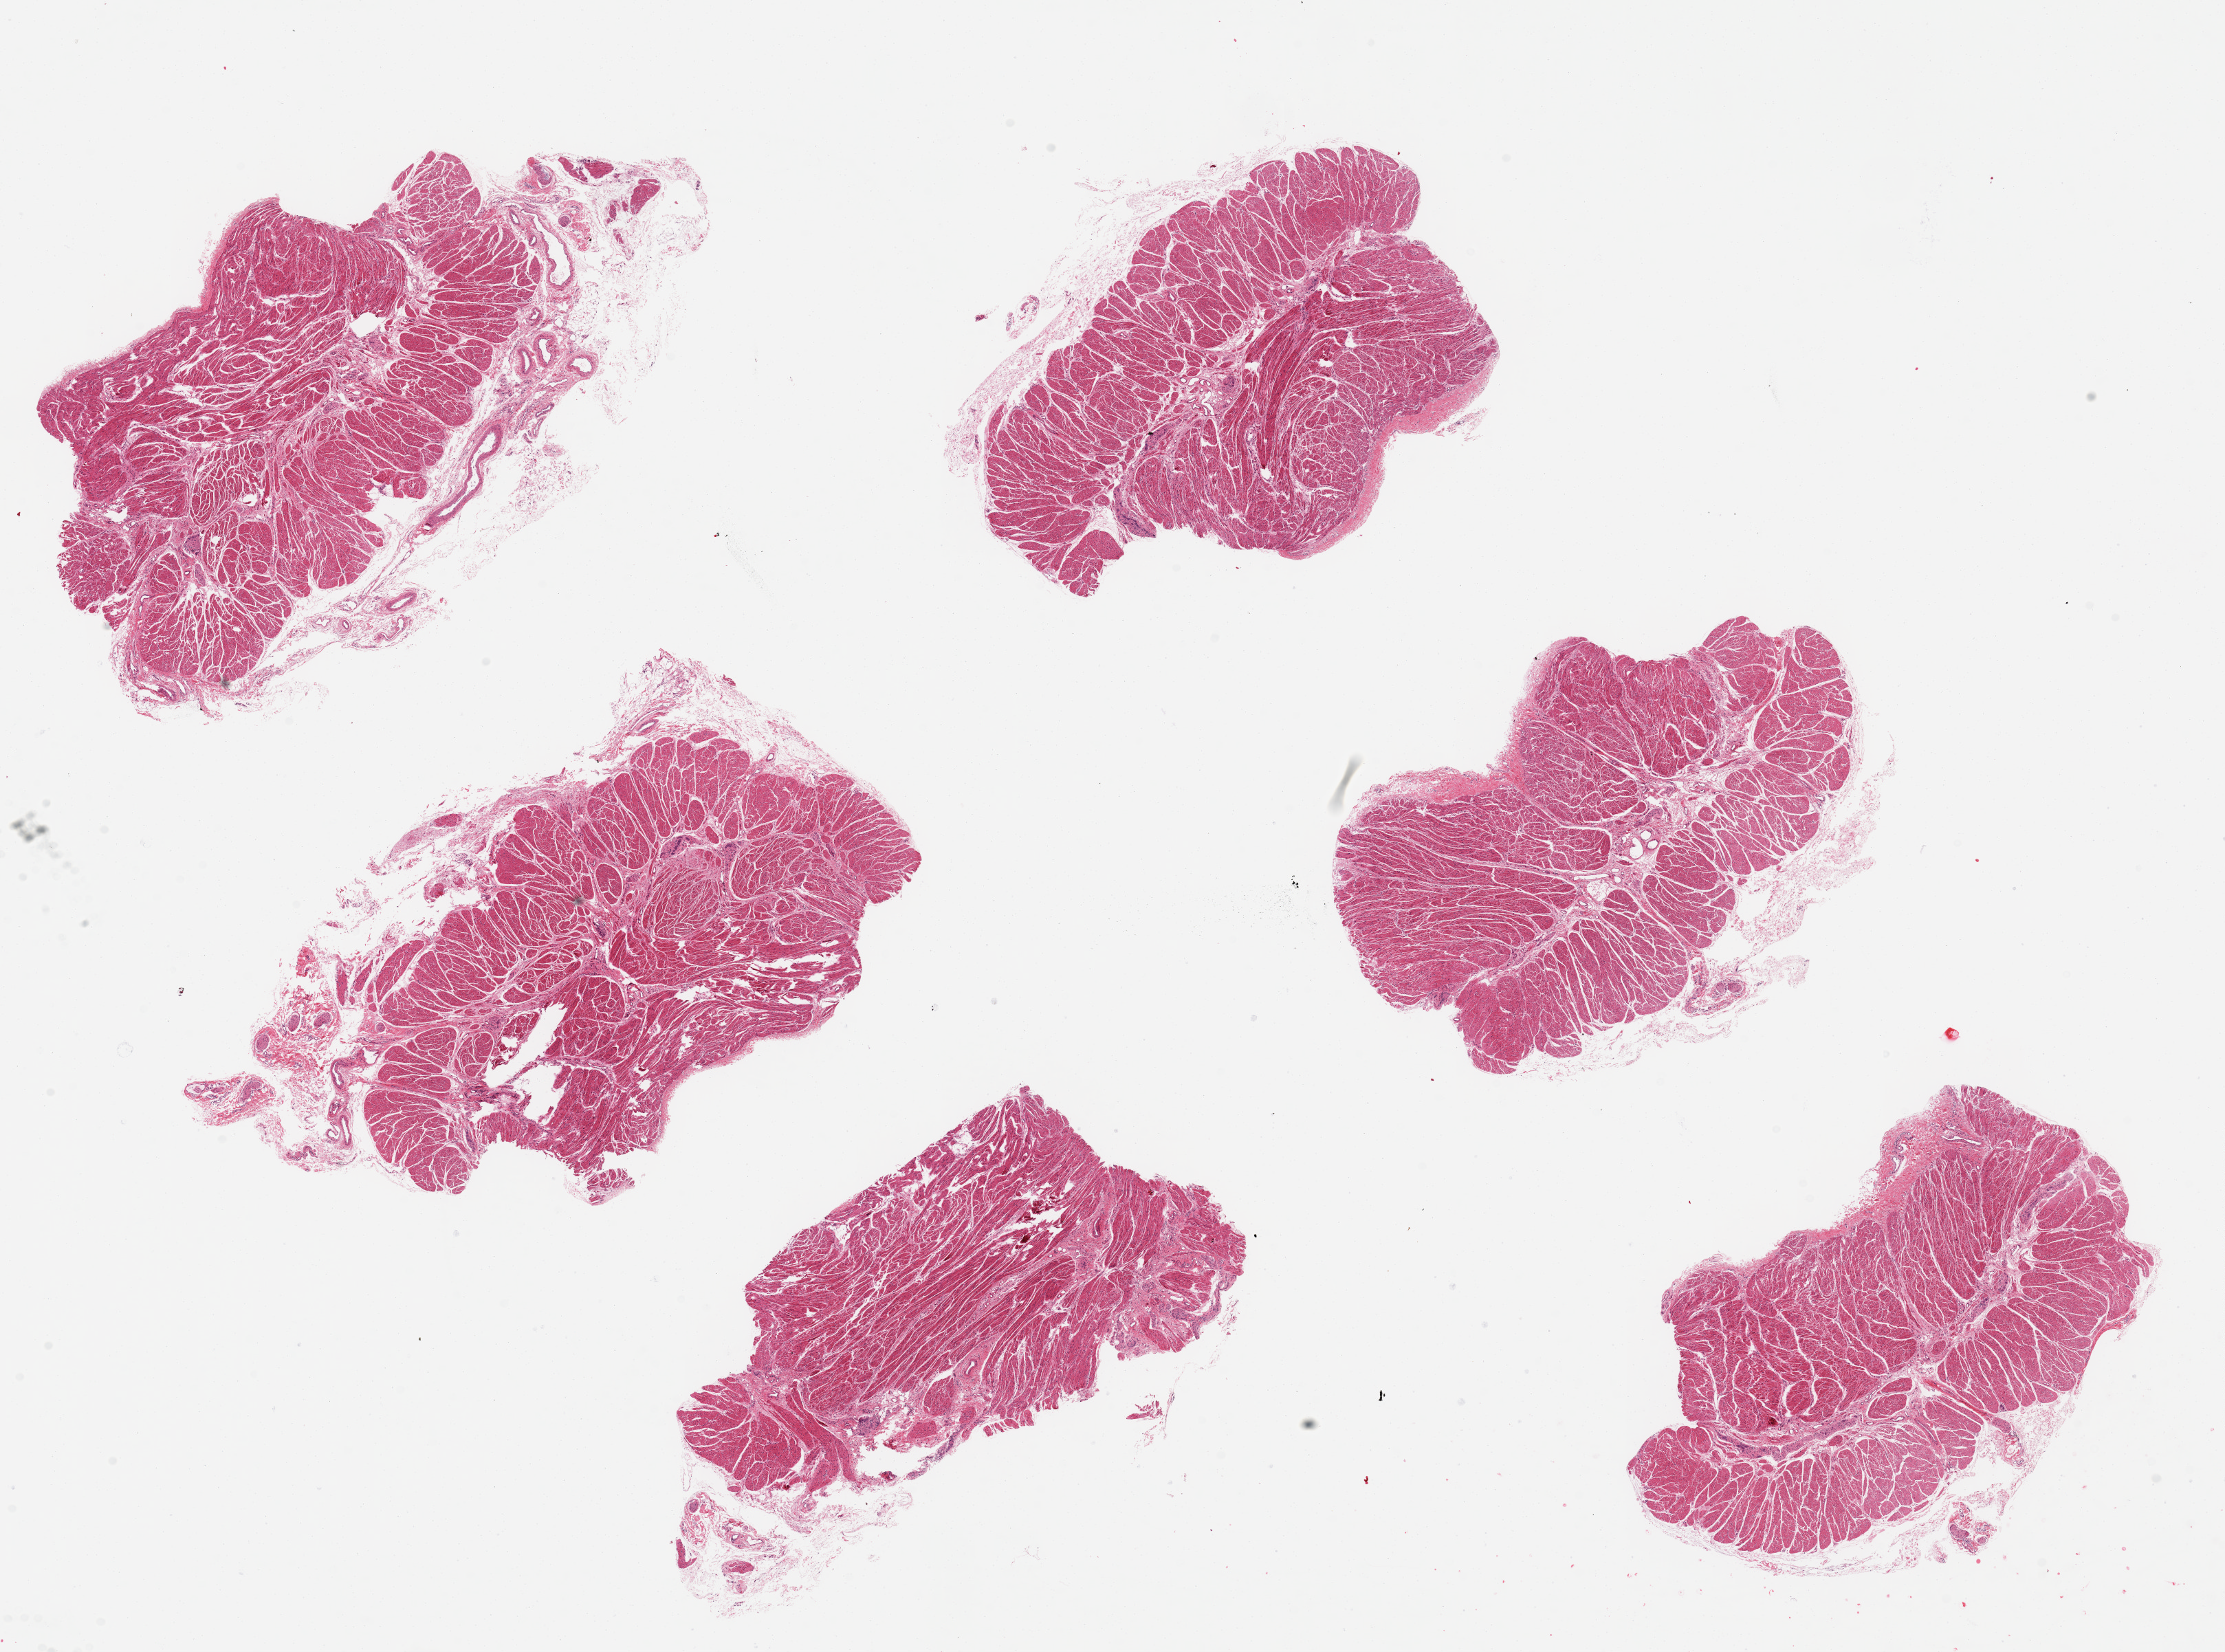
Digitized H&E-stained section, whole scanned area (about 25.6 x 19.0 mm) shown as a low-resolution overview; PAXgene-fixed, paraffin-embedded tissue; section of esophageal muscle (target tissue); tissue donor sample. Donor: female.
Review note (as recorded): 6 pieces, up to 7.7x4 mm.